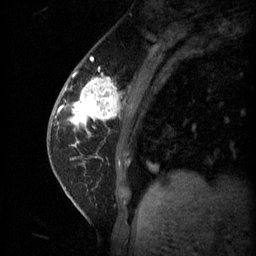
Breast MRI (dynamic contrast-enhanced), one sagittal slice; position 16 of 60 along the scan axis; 3 images stored at this slice position (order not interpretable as contrast timing); 1.5 T; TE 4.2 ms, TR 11 ms; 256 × 256 image matrix, field of view 180 × 180 mm. Female patient, age 62 years.
Outlined on this slice (semi-automatically segmented with operator editing):
- analysis volume of interest (the breast-tissue region the enhancement analysis was run in; not a lesion): bounding box (x1, y1, x2, y2) in pixels: (55, 72, 124, 133)
- tumour enhancement mask (voxels above the 70 % enhancement threshold inside the analysis volume of interest): (60, 74, 121, 129)